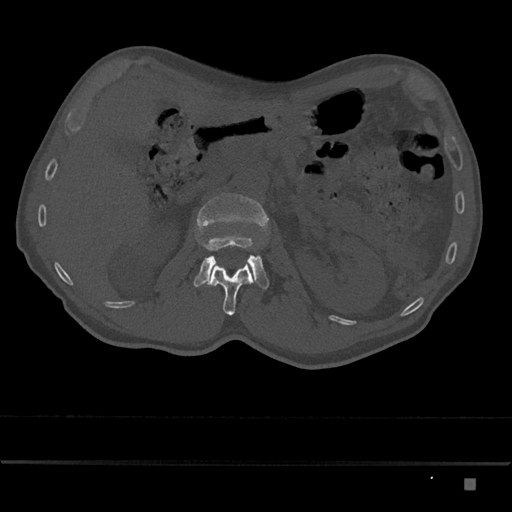
CT including the spine, one axial slice. Position 514 of 797 along the scan axis. 120 kVp. Bone window (W 1800 / L 400 HU). 0.5 mm slice thickness. 512 × 512 image matrix. Male patient, age 72 years. From the clinical record (not read from this slice): primary cancer: prostate.
Outlined on this slice (semi-automatically segmented with operator editing):
- L1 vertebra: box from (x=207, y=262) to (x=255, y=315) px
- L2 vertebra: (x=193, y=193)–(x=270, y=289)